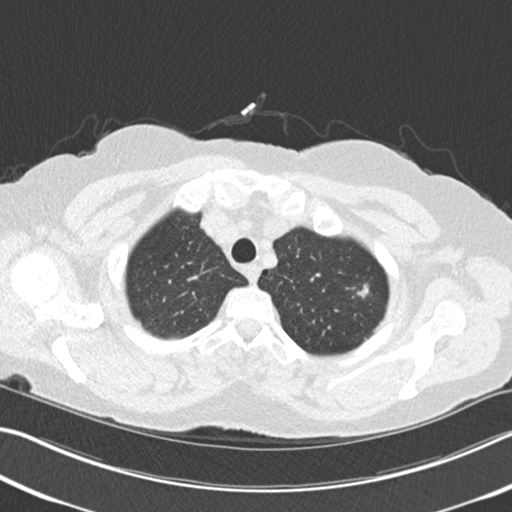
Low-dose screening chest CT, axial slice, second screening round (one year after baseline), lung window (W 1500 / L -600 HU), 2 mm slice thickness, standard (soft-tissue) reconstruction kernel (B30f), 512 × 512 image matrix. Female, age 64 years at enrolment. Former smoker at enrolment.
- Lesion marked by an expert reader, bounding box <344,274,377,306> (left, top, right, bottom; pixels).
- The exam's reader record, not a measurement of the box and not confirmed to be the same lesion: non-calcified nodule or mass ≥4 mm, left upper lobe, 13 × 10 mm, spiculated (stellate) margins, soft tissue attenuation, pre-existing on the prior screen: yes; interval growth: yes.
- Lung cancer was diagnosed 106 days after this screen: signet ring cell carcinoma, right upper lobe, poorly differentiated (G3), stage IA (AJCC 6th edition), 15 mm at pathology.